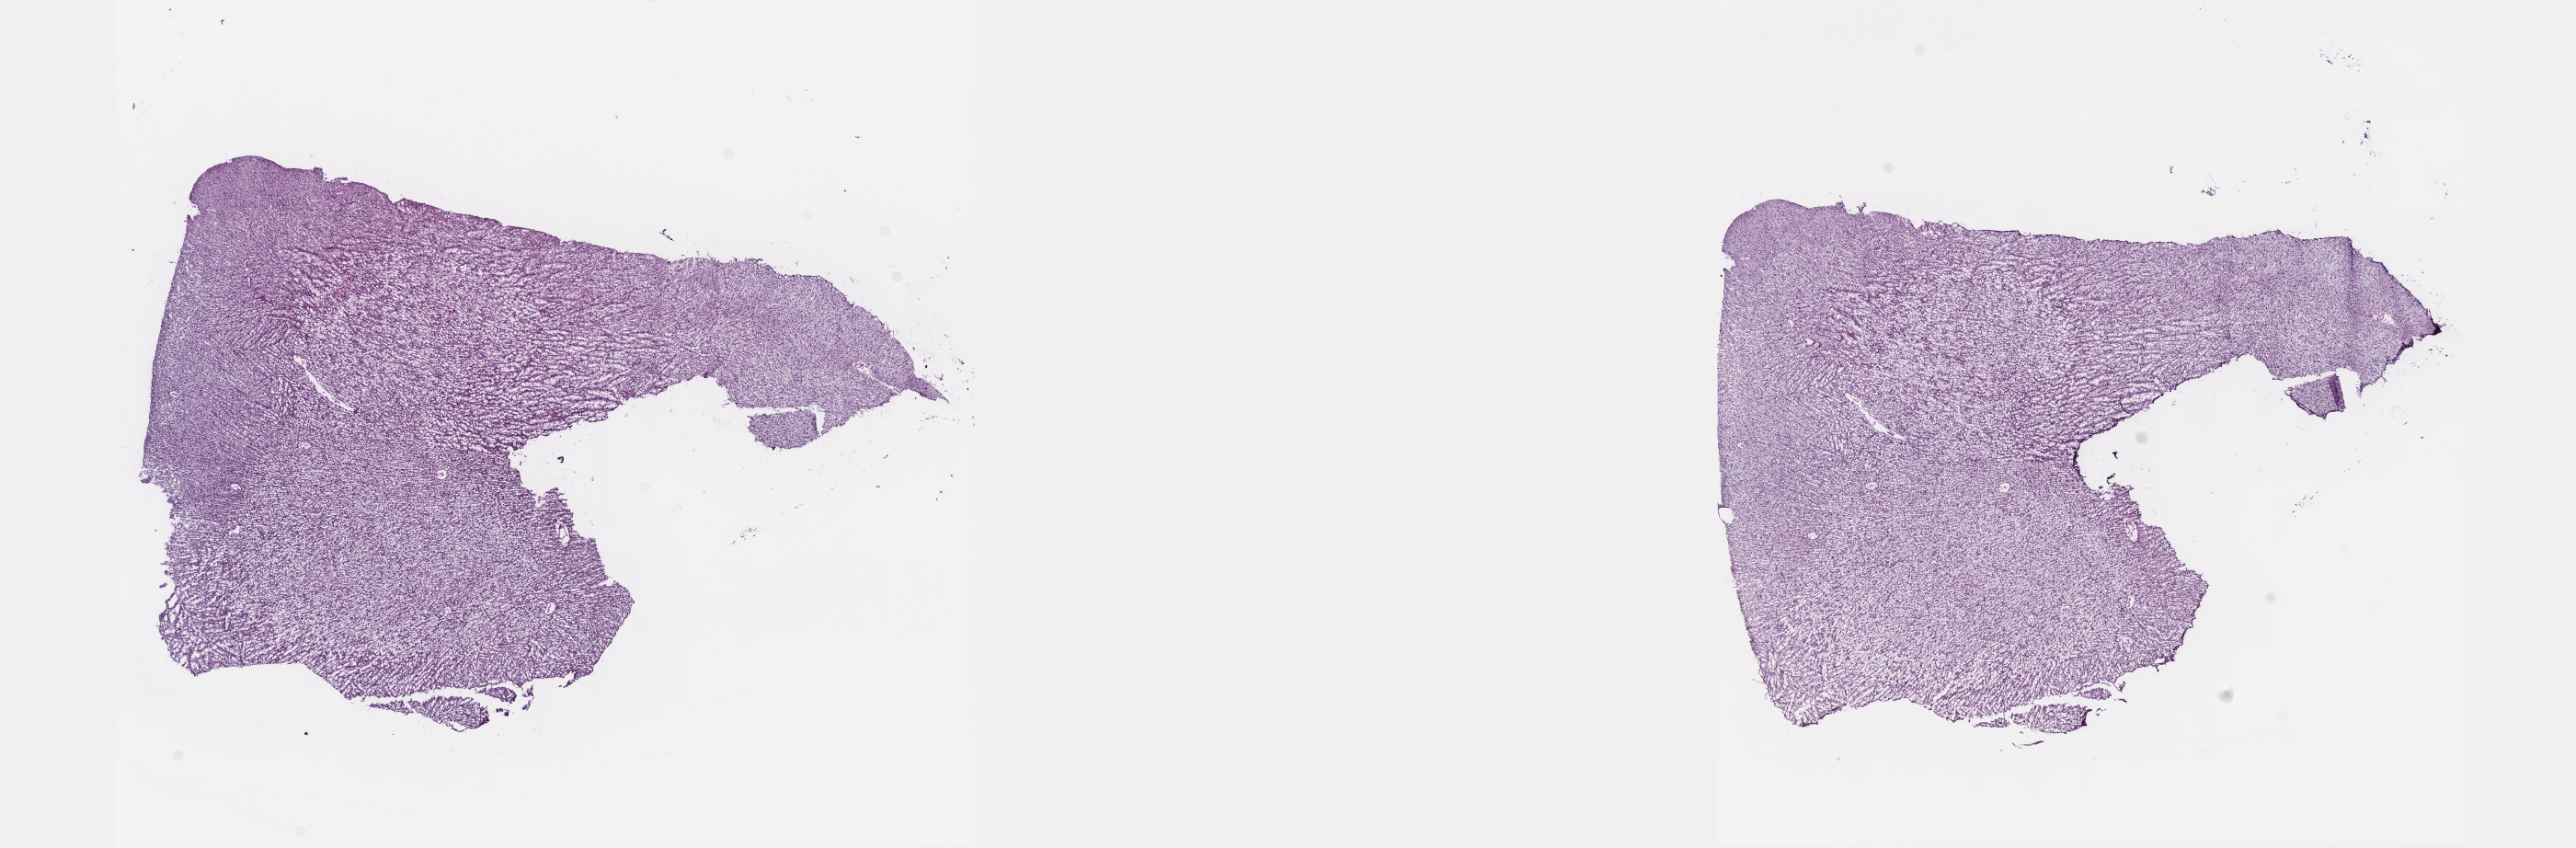
Whole-slide histology image, Hematoxylin and eosin (H&E) stained — low-resolution overview of the scanned area, about 22.6 x 7.5 mm, frozen section, sample: primary tumour, brain. Female patient; age at initial diagnosis 38 years. Histologic grade: G3 (poorly differentiated). Composition of this section per pathologist review: tumour cells 50%, tumour nuclei 85%, normal cells 10%, stromal cells 40%, necrosis 0%. Infiltration values recorded for this section: lymphocyte infiltration 0%, monocyte infiltration 0%, neutrophil infiltration 0%.
Histologic diagnosis: Mixed glioma (cerebrum). Laterality: right.